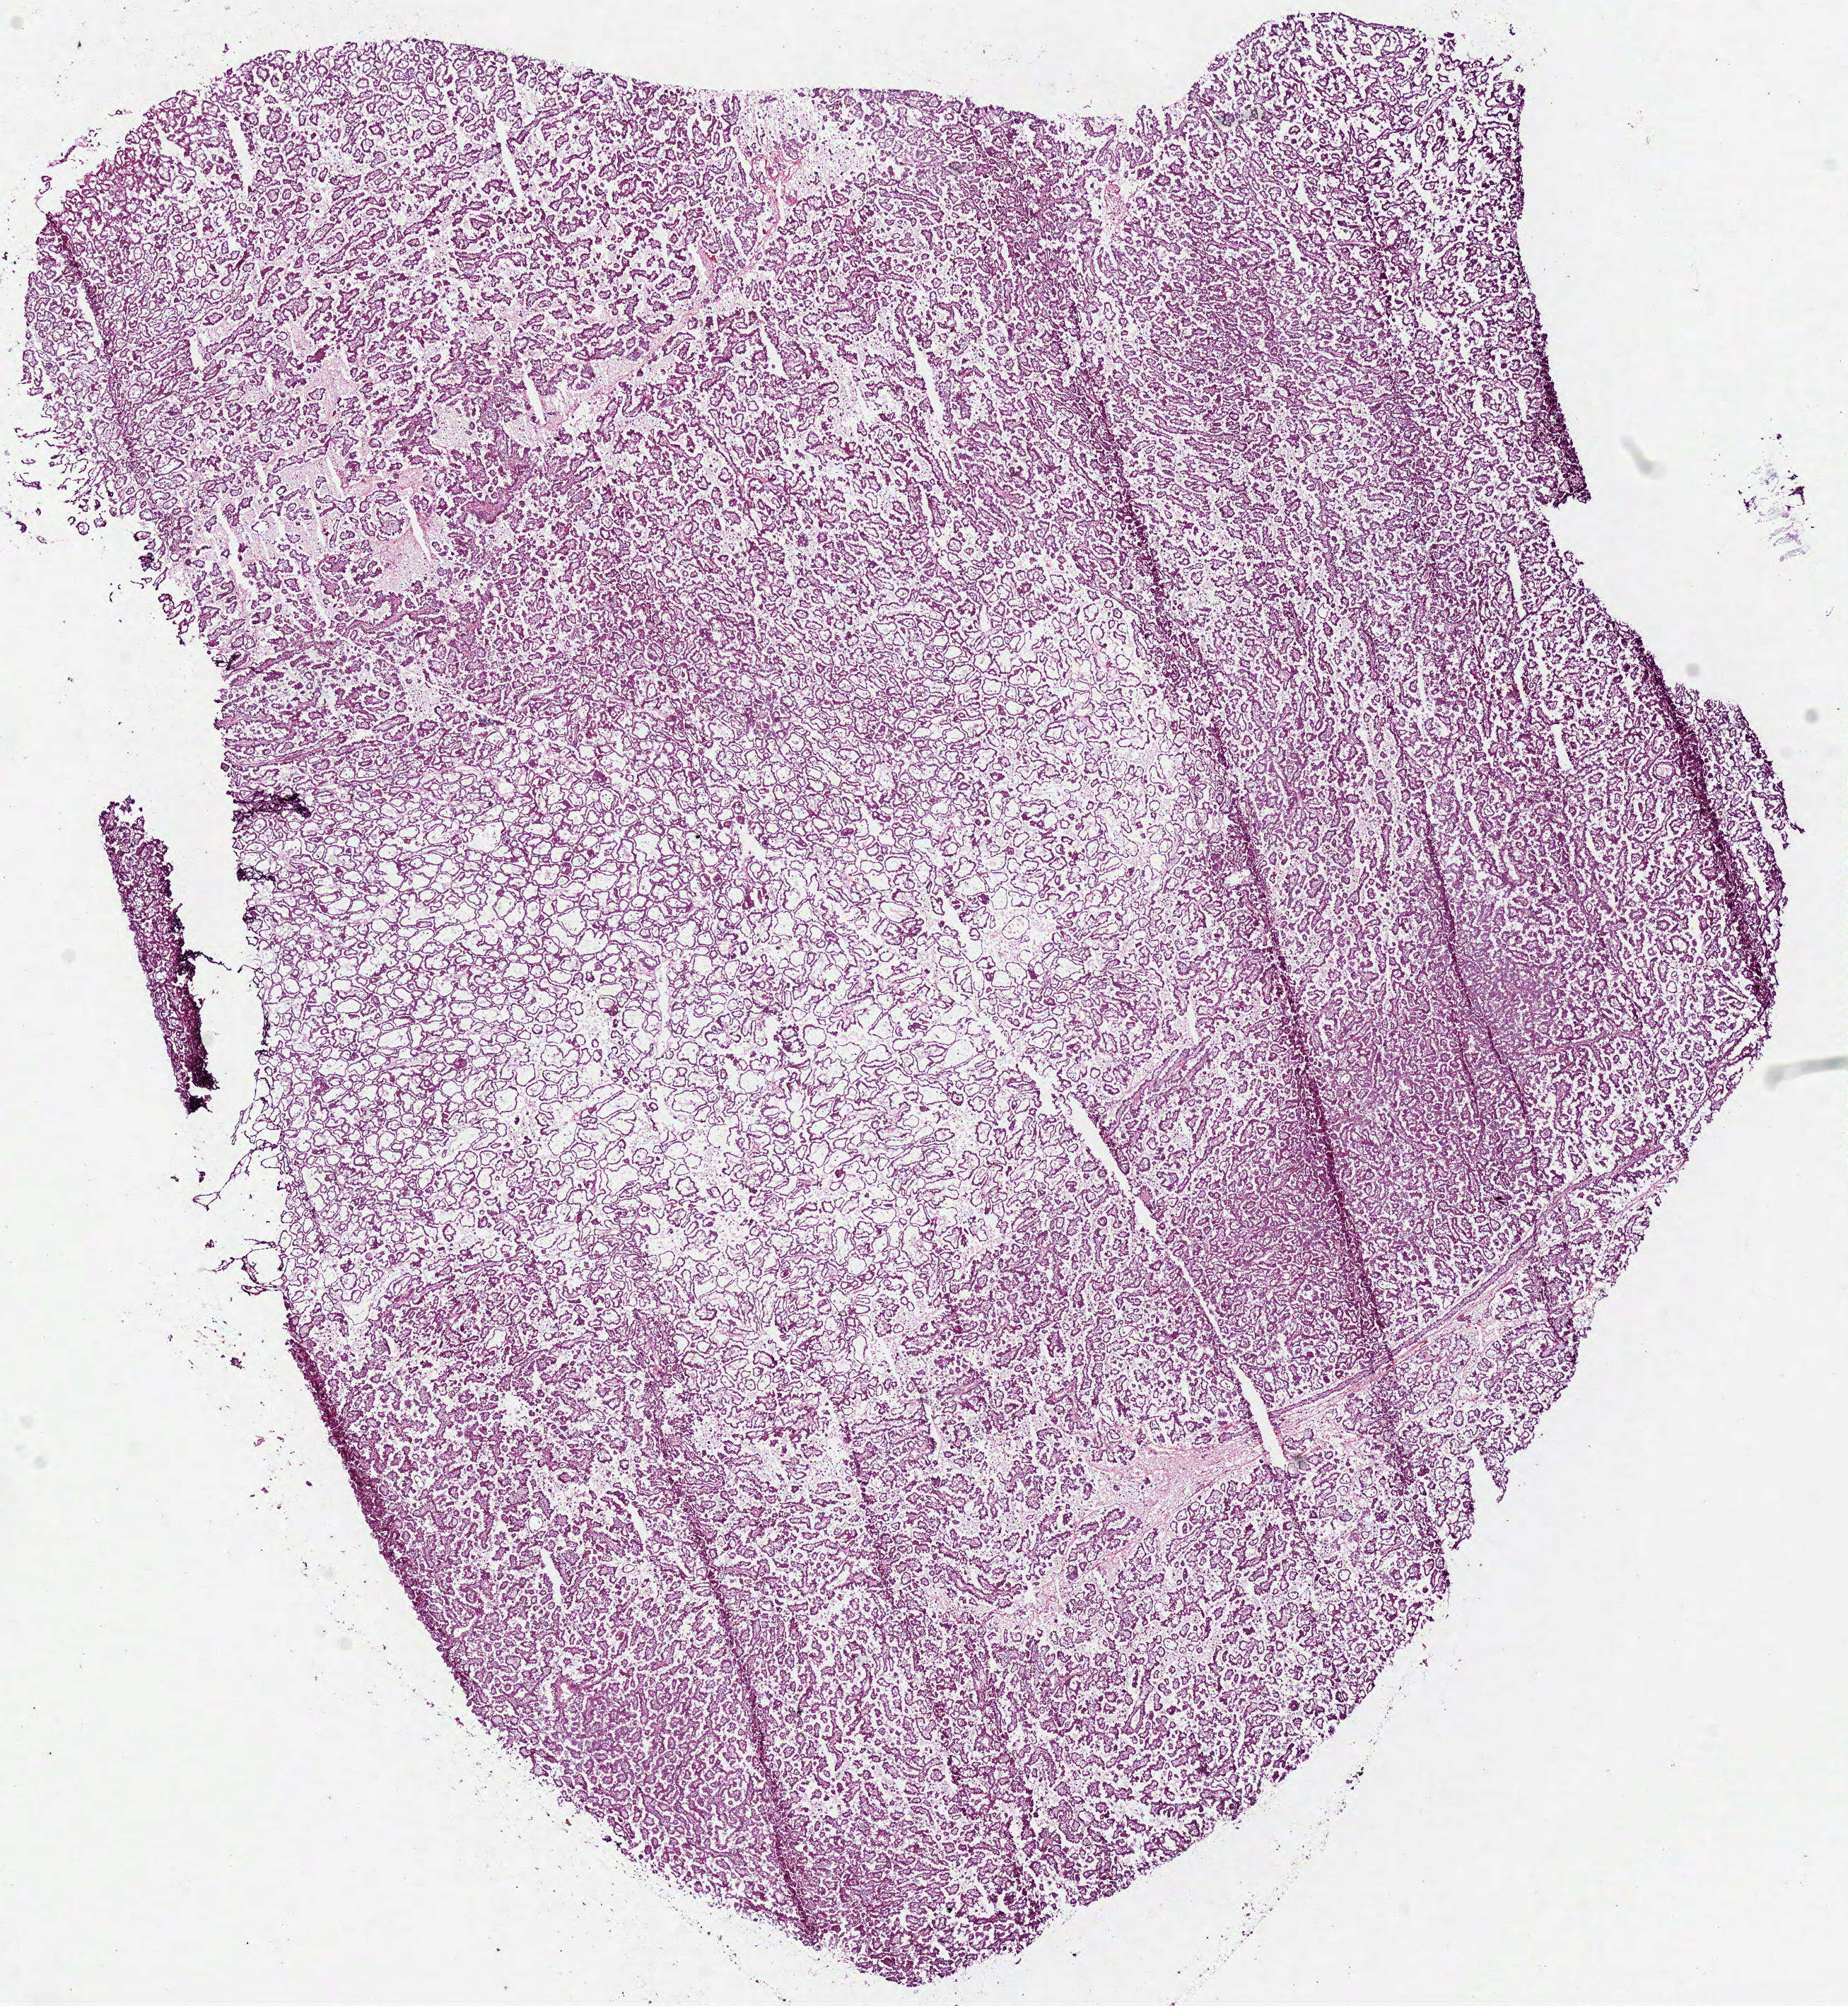
H&E whole-slide image, low-resolution overview of the scanned area, about 10.3 x 11.2 mm. Frozen section. Primary tumour sample from the kidney. Patient: male, age at initial diagnosis 40 years. Composition of this section per pathologist review: tumour cells 100%, tumour nuclei 90%, normal cells 0%, stromal cells 0%, necrosis 0%.
Histologic diagnosis: Papillary adenocarcinoma, NOS. AJCC pathologic stage: I.